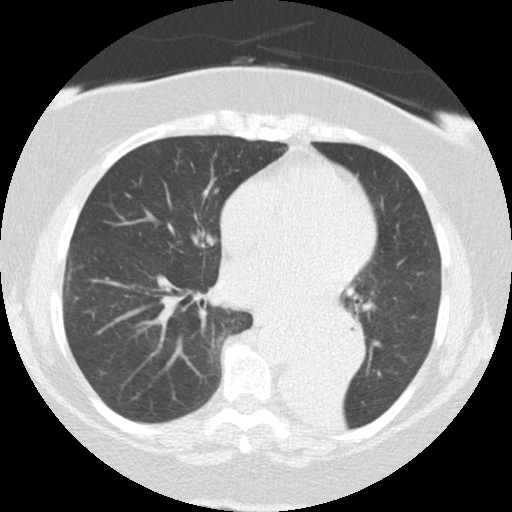
Low-dose screening chest CT, axial slice; first (baseline) screen; lung window (W 1500 / L -600 HU); 2.5 mm slice thickness; standard (soft-tissue) reconstruction kernel (STANDARD); 120 kVp; slice 72 of 136 in the series. Female, age 71 years at enrolment.
Expert-annotated lung lesion, bounding box <282,304,367,383> (left, top, right, bottom; pixels). Reader record for this screening exam (exam-level; its link to the box is not recorded): non-calcified nodule or mass ≥4 mm, right middle lobe, 5 × 5 mm, smooth margins, soft tissue attenuation. Note: the box lies in the patient's left hemithorax on this image, whereas the reader's record names the right lung; they may be different findings. Official screen result: positive, change unspecified: nodule(s) >= 4 mm or enlarging nodule(s), mass(es), or other non-specific abnormalities suspicious for lung cancer.